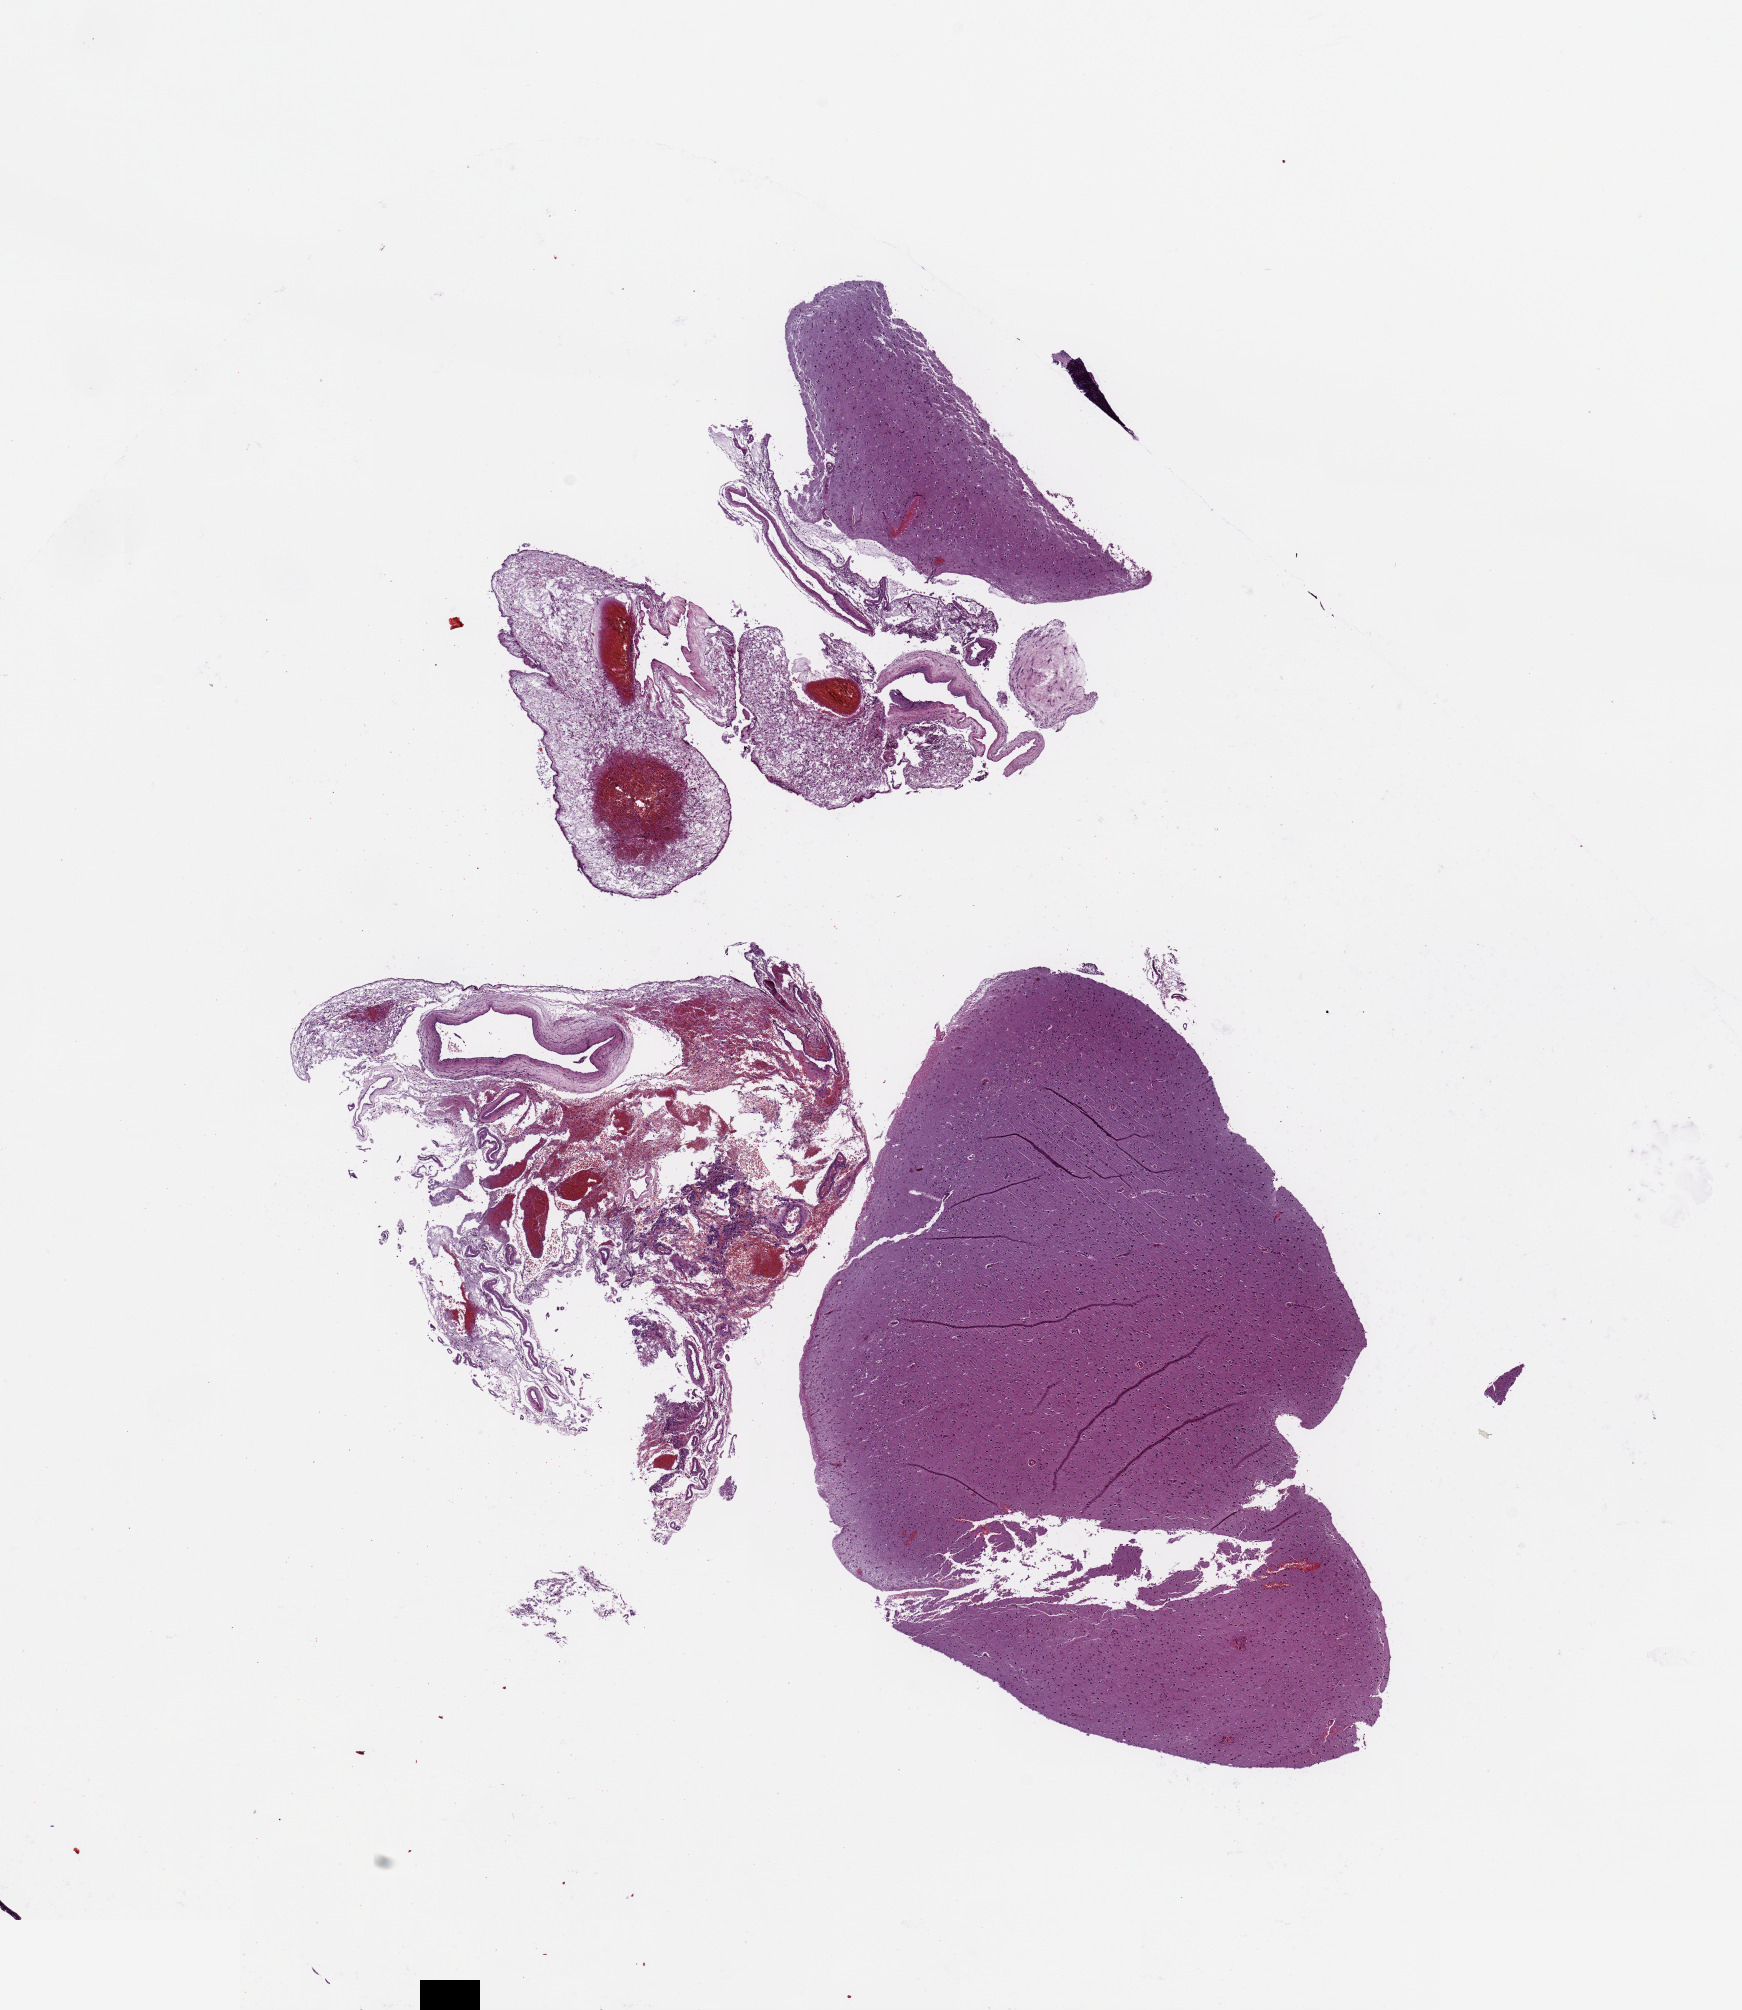
Digitized H&E tissue section (whole slide), a low-resolution overview of the entire scanned area, about 13.8 x 15.9 mm (acquisition: 20x scan), tumour tissue sample, brain. Male, 70 y/o.
Histologic diagnosis: Glioblastoma.